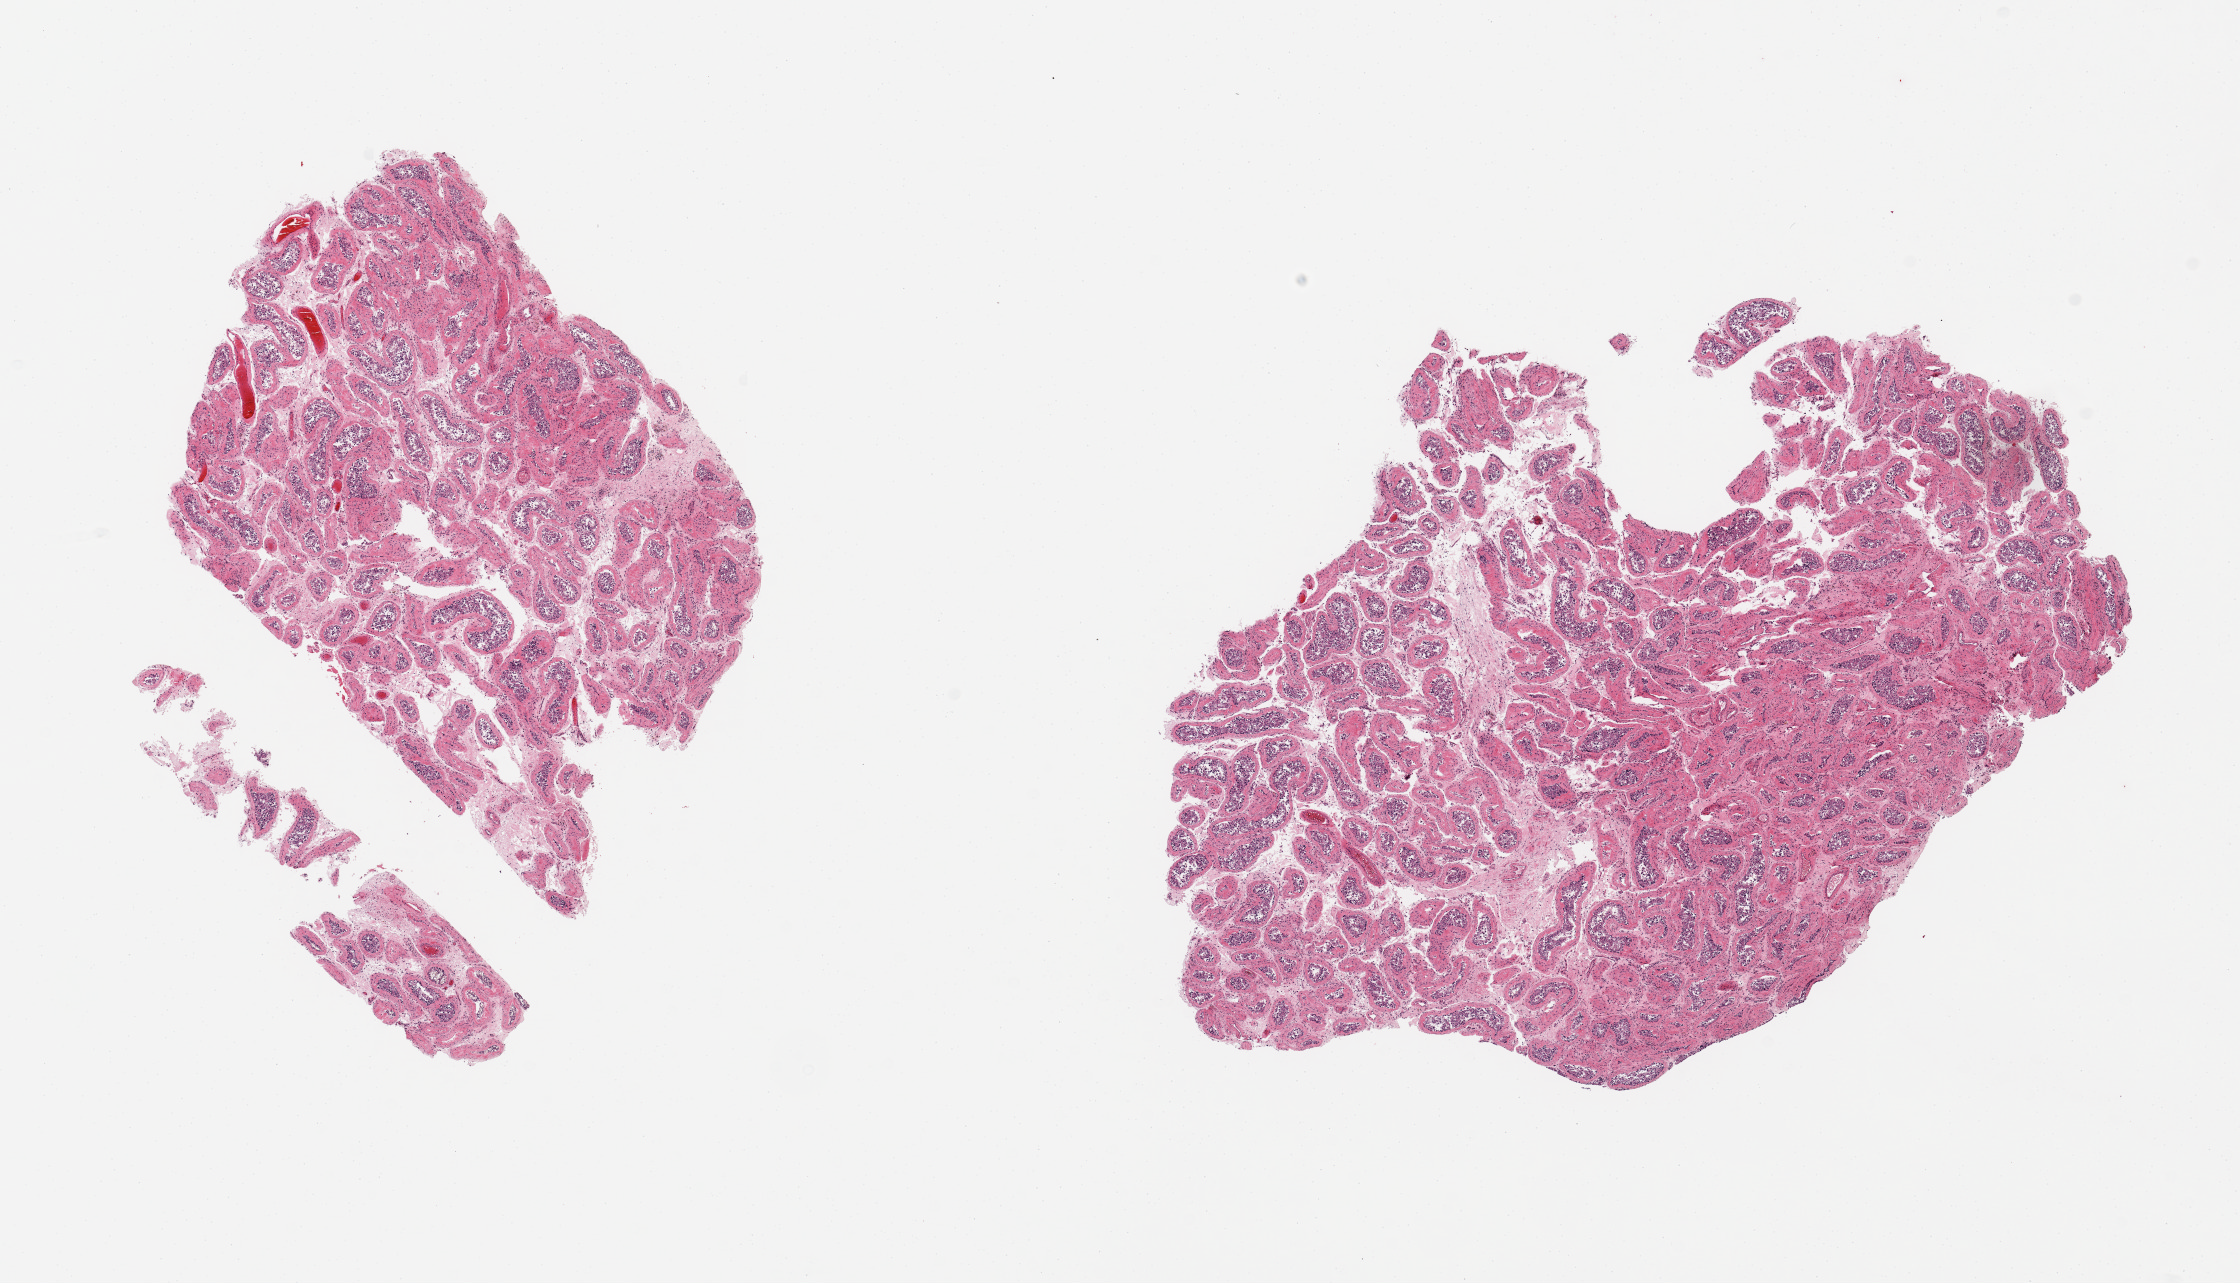
Hematoxylin and eosin (H&E) whole-slide image, brightfield, a low-resolution overview of the entire scanned area, about 17.7 x 10.1 mm; PAXgene-fixed paraffin-embedded (PFPE) section; target tissue: testis; tissue donor sample. Donor: male.
Review note (as recorded): 2 pieces, spermatogenesis appears markedly reduced, moderate-marked autolysis.